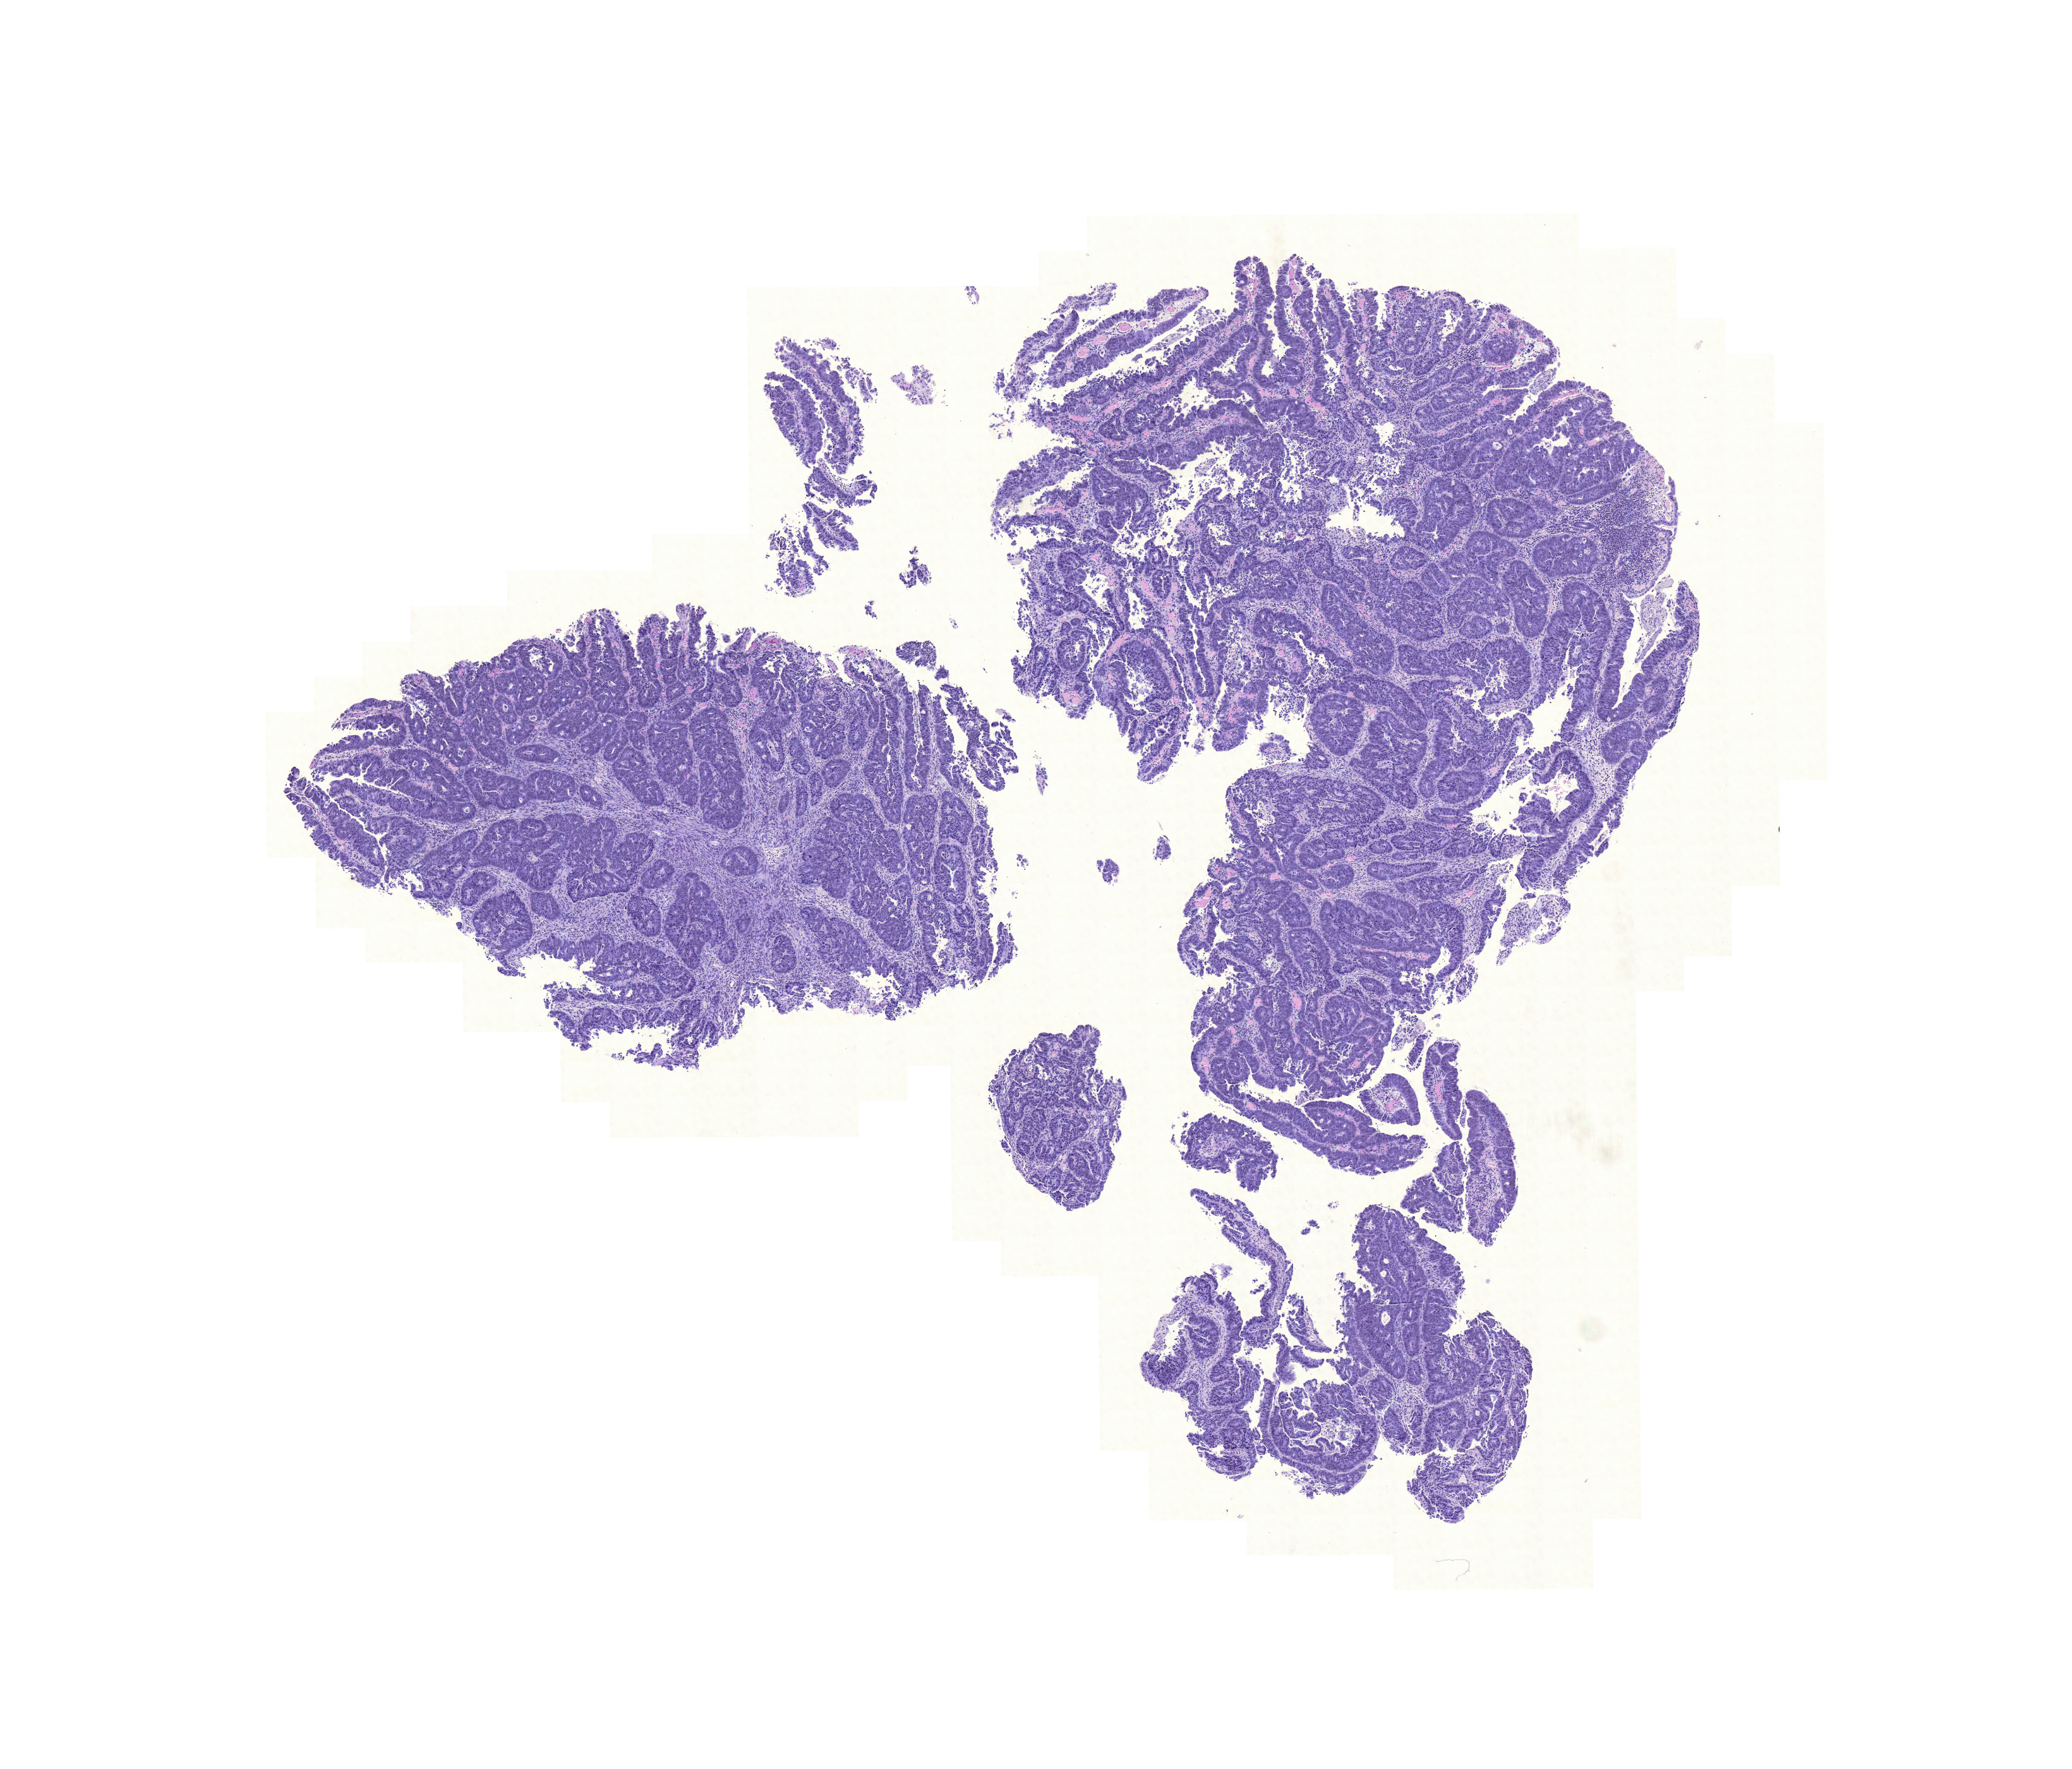
Whole-slide histology image, Hematoxylin and eosin (H&E) stained, shown as a low-resolution overview of the whole scanned area (about 12.2 x 10.4 mm). Formalin-fixed paraffin-embedded (FFPE) diagnostic section. Sample: primary tumour, colon. Patient: male, age at initial diagnosis 63 years.
- histologic diagnosis: Mucinous adenocarcinoma (cecum)
- TNM: T3 N0 M0
- AJCC pathologic stage: IIA